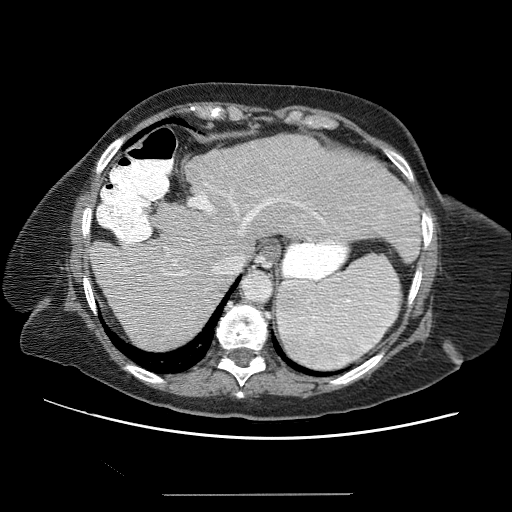
Contrast-enhanced abdominal CT (liver protocol), one axial slice; slice 46 of 65 in the series (ordered by position); soft-tissue window (W 400 / L 40 HU); 2.5 mm slice thickness; 512 × 512 image matrix. Case-level facts recorded for this patient, not image findings: diagnosis: hepatocellular carcinoma (patient treated with transarterial chemoembolisation; whether this scan precedes or follows treatment is not stated here); TNM stage (as recorded): Stage-IIIB; Child-Pugh class: A; tumour differentiation: moderately differentiated.
Outlined on this slice (semi-automatic segmentation, software-assisted and operator-edited):
- liver parenchyma outside the tumour (the mass and vessels are separate outlines, so this box may not span the whole liver): box from (x=90, y=136) to (x=423, y=344) px
- mass: (x=154, y=242)–(x=191, y=275)
- liver vessels: (x=105, y=157)–(x=411, y=329)